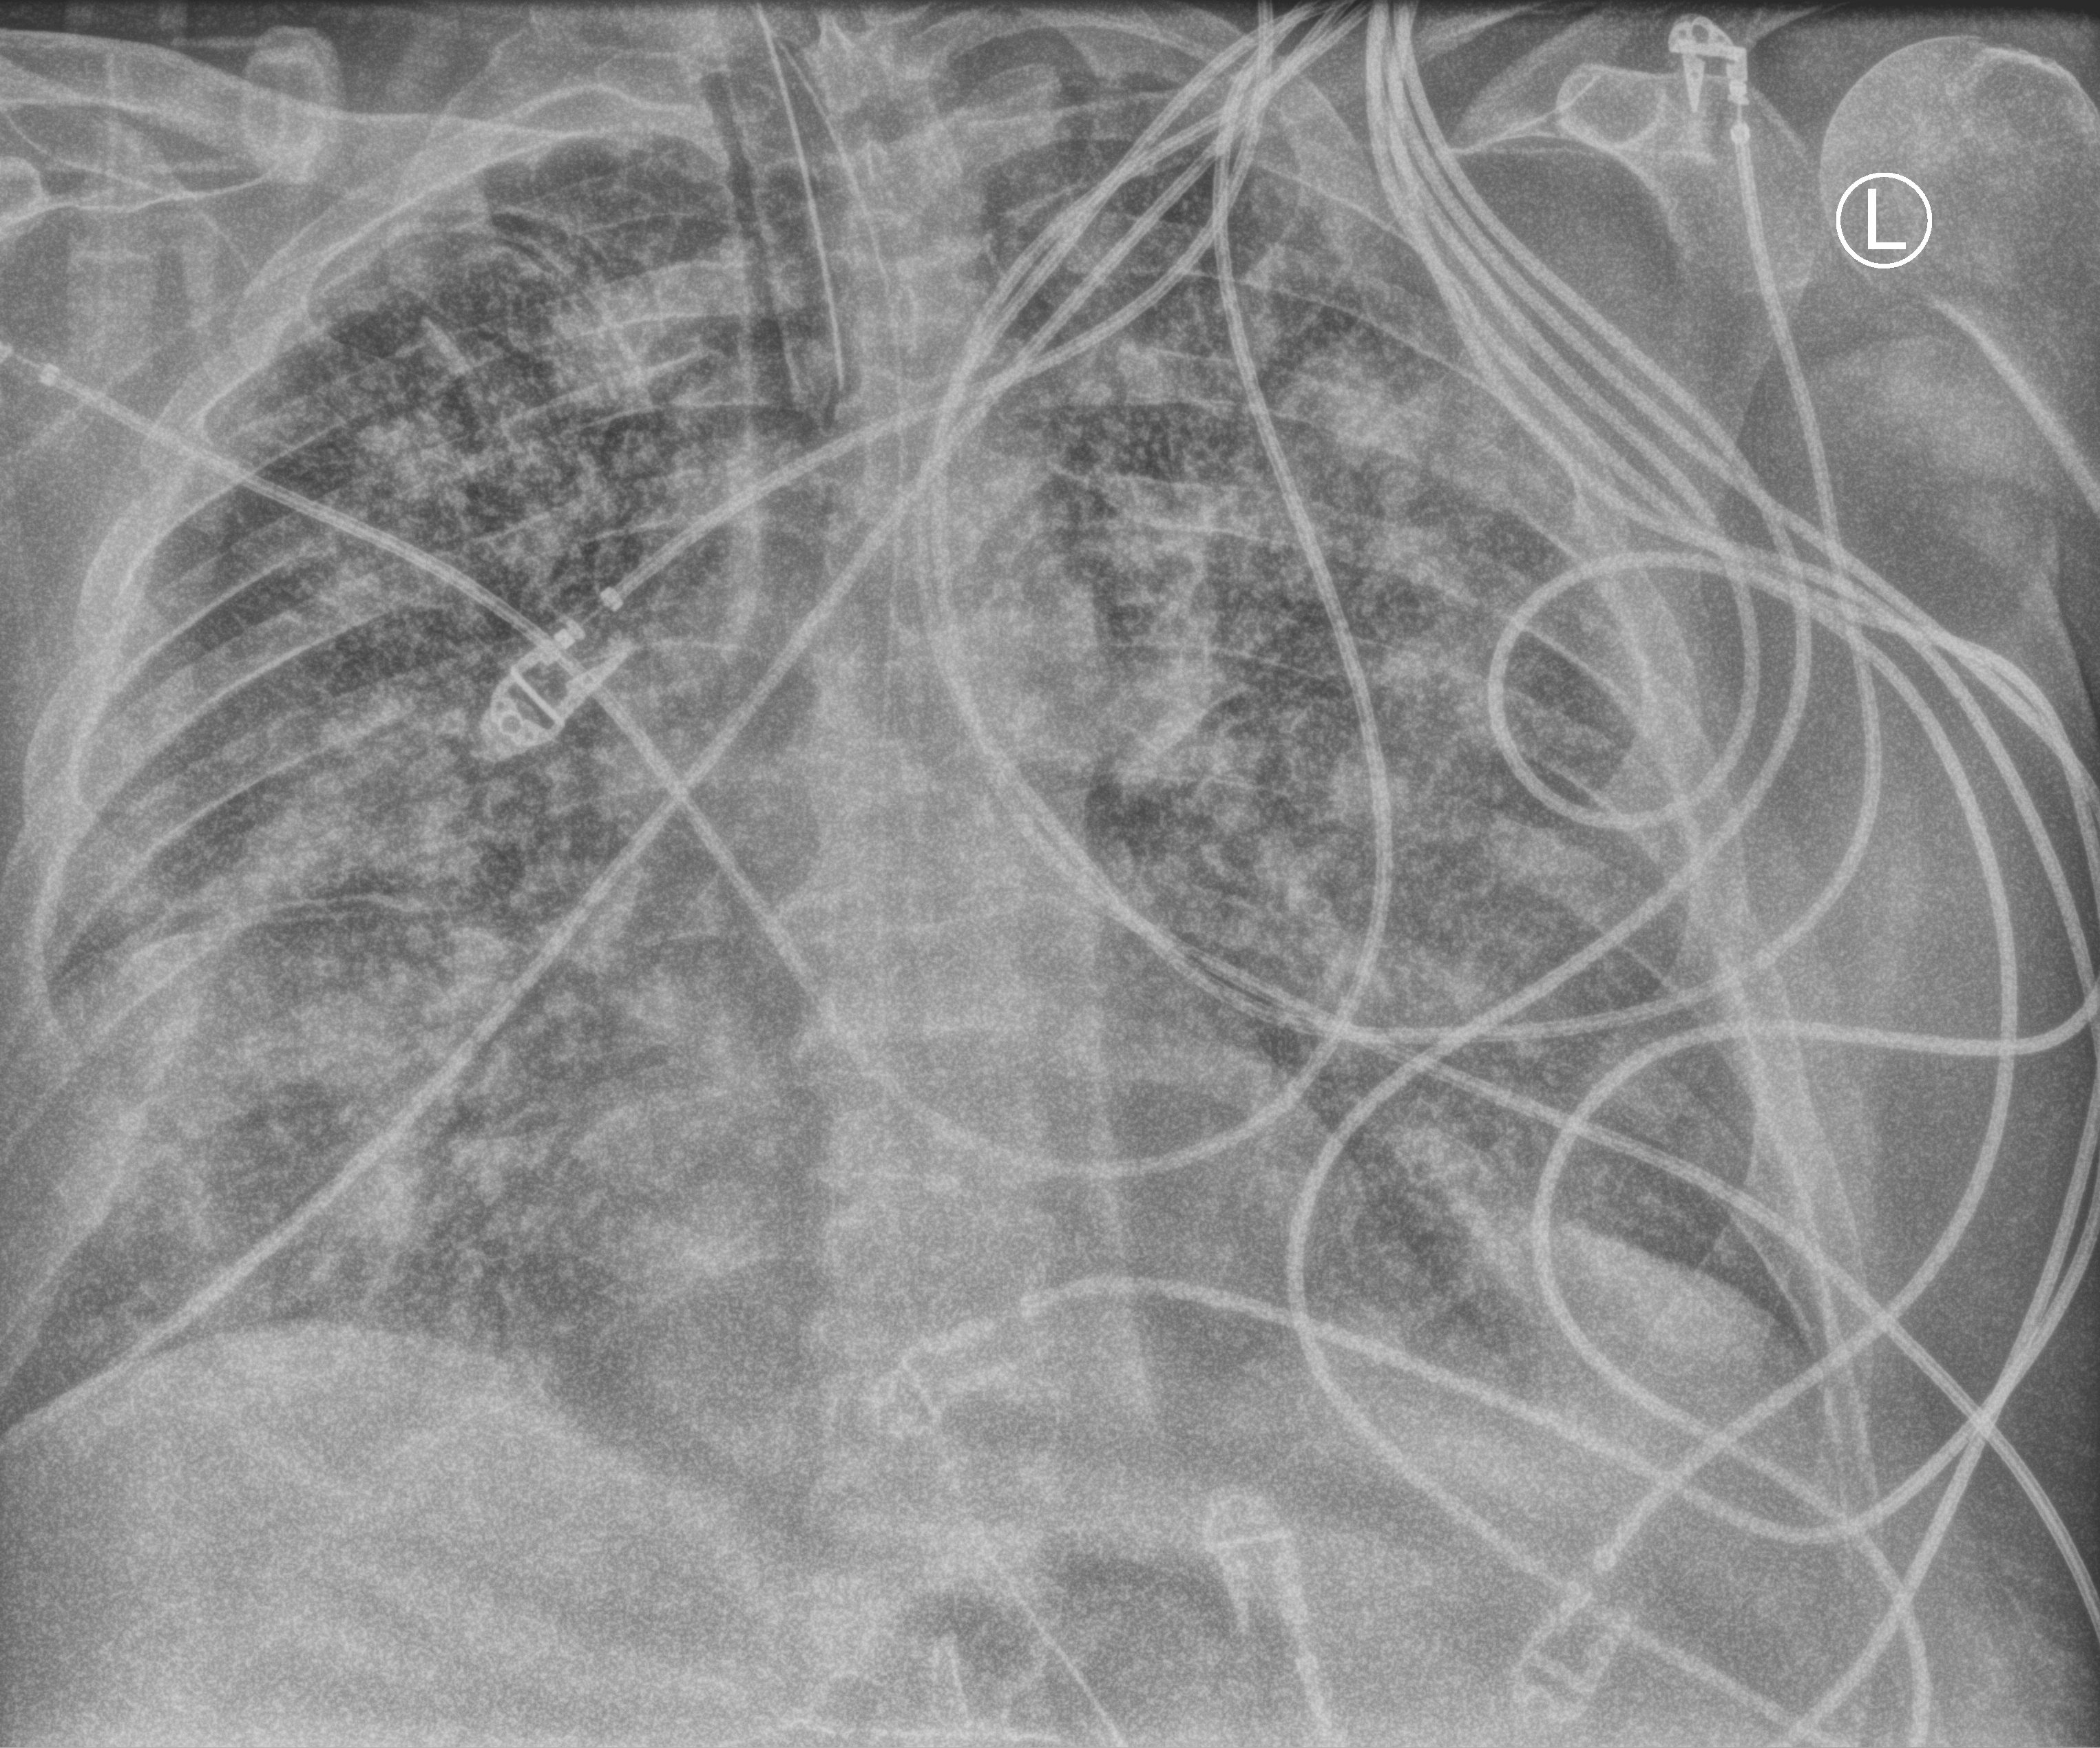
Portable chest radiograph; anteroposterior (AP) projection. Male patient hospitalised with COVID-19, age 60–74 years.
Hospital-stay facts (about this admission, not read from this image; timing relative to this image not recorded): mechanically ventilated during this hospital stay: yes; chronic kidney disease (admission record): no.